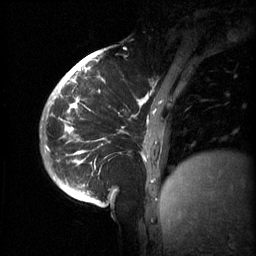
Breast MRI (dynamic contrast-enhanced), one sagittal slice. Position 14 of 60 along the scan axis. 3 images stored at this slice position (order not interpretable as contrast timing). 1.5 T. TE 4.2 ms, TR 11 ms. 2 mm slice thickness. 256 × 256 image matrix, field of view 220 × 220 mm. Female patient, age 51 years.
Annotated regions visible in this slice (semi-automatically segmented with operator editing):
- analysis volume of interest (the breast-tissue region the enhancement analysis was run in; not a lesion): bounding box (x1, y1, x2, y2) in pixels: (63, 80, 186, 201)
- tumour enhancement mask (voxels above the 70 % enhancement threshold inside the analysis volume of interest): (68, 80, 169, 189)